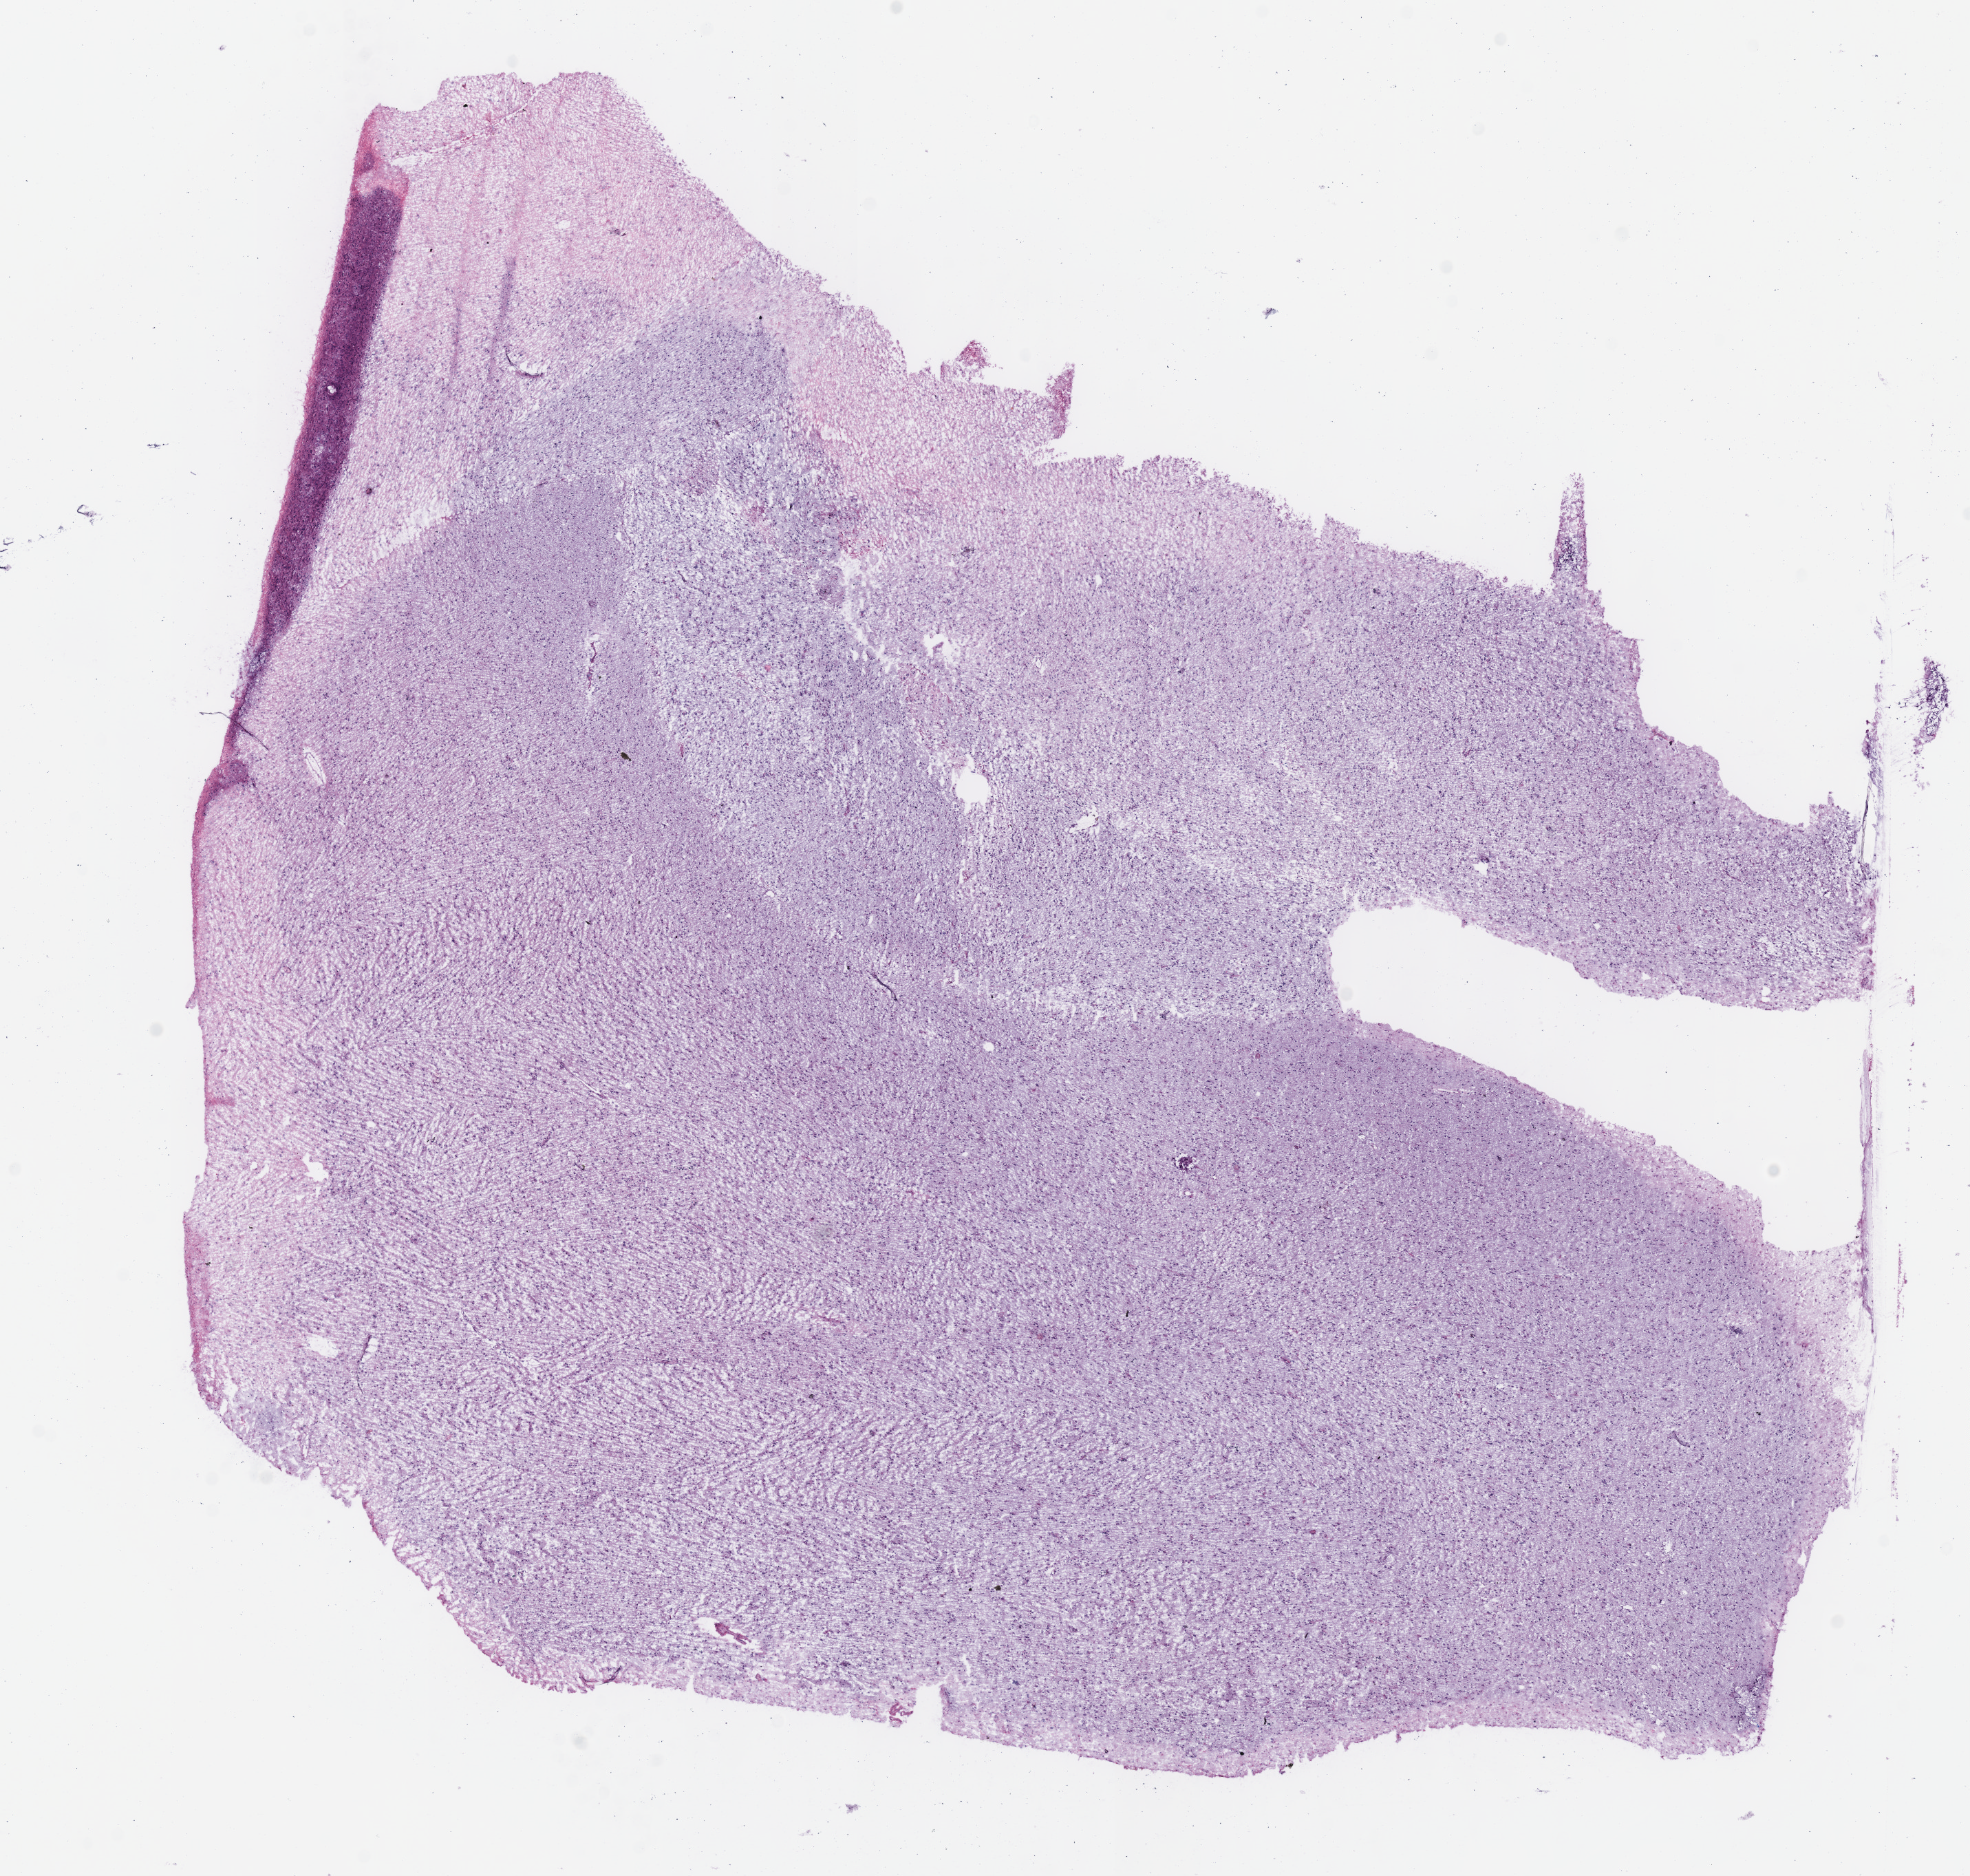
Digitized Hematoxylin and eosin (H&E) stained tissue section (whole slide) — low-resolution overview of the scanned area, about 11.3 x 10.7 mm (slide scanned at 40x). Frozen section from the bottom of the tissue portion. Sample: primary tumour, brain. Female patient; age at initial diagnosis 34 years. Histologic grade: G3 (poorly differentiated). Slide review estimates, as recorded: tumour cells 100%, tumour nuclei 75%, normal cells 0%, stromal cells 0%, necrosis 0%.
- pathologic diagnosis: Astrocytoma, anaplastic (cerebrum)
- laterality: left